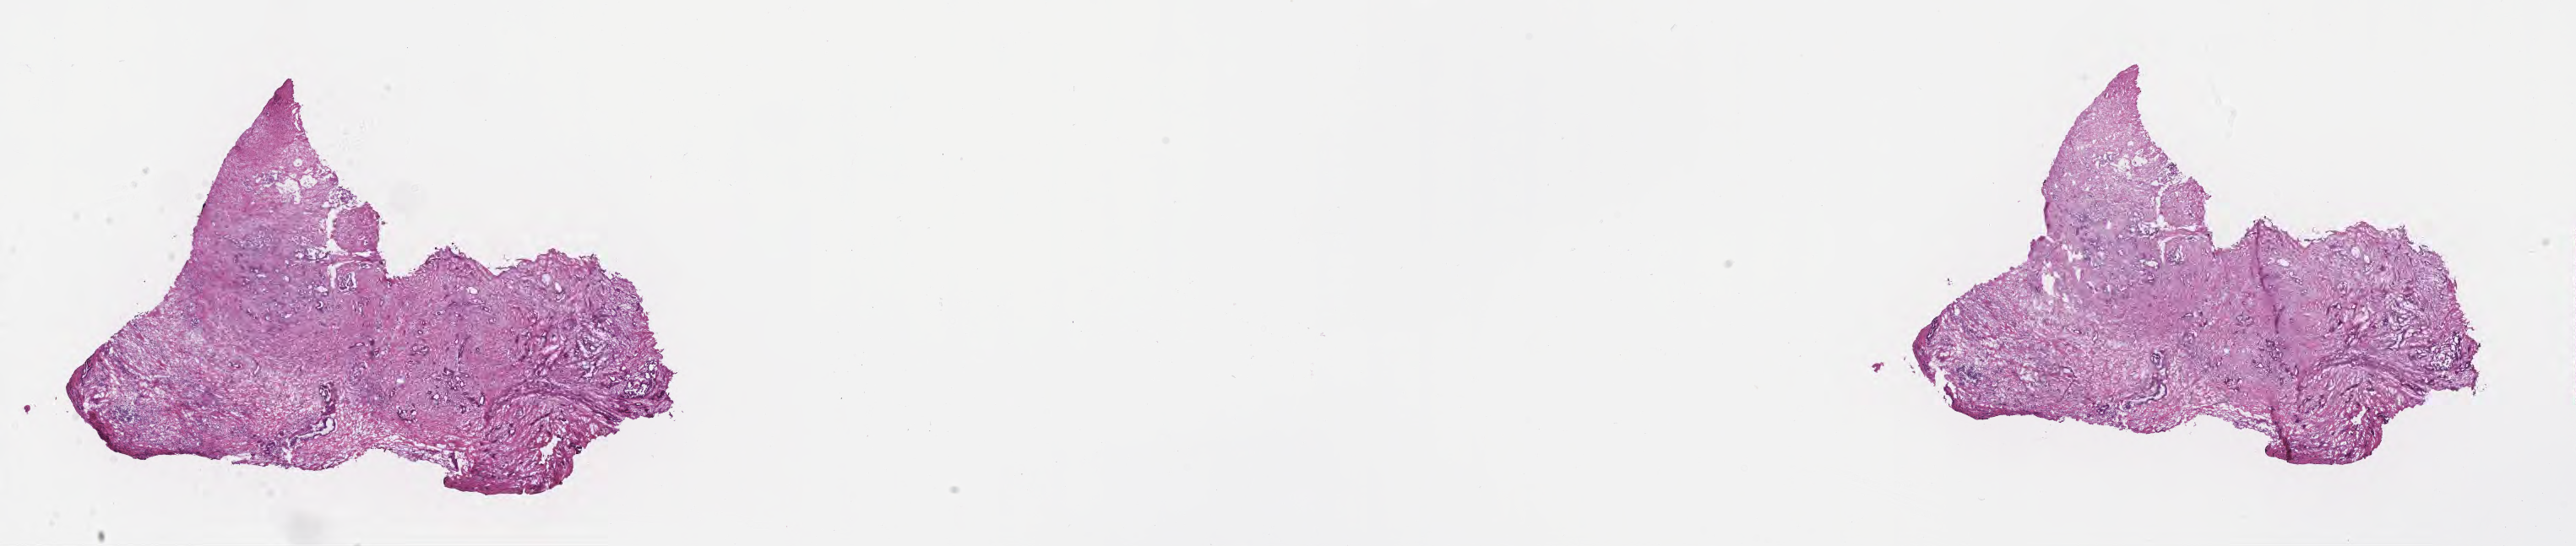
Digitized hematoxylin and eosin (H&E)-stained section, low-resolution overview of the scanned area, about 24.7 x 5.2 mm, frozen section, specimen: primary tumor, anatomic site: tail of pancreas. Patient: female, age at initial diagnosis 70 years. Pathologist review of this section (percent, as recorded): tumor cells 16%, tumor nuclei 70%, stromal cells 82%, necrosis 2%, normal cells 0%. Infiltration values recorded for this section: lymphocyte infiltration 6%, monocyte infiltration 1%, neutrophil infiltration 0%.
- diagnosis: Infiltrating duct carcinoma, NOS